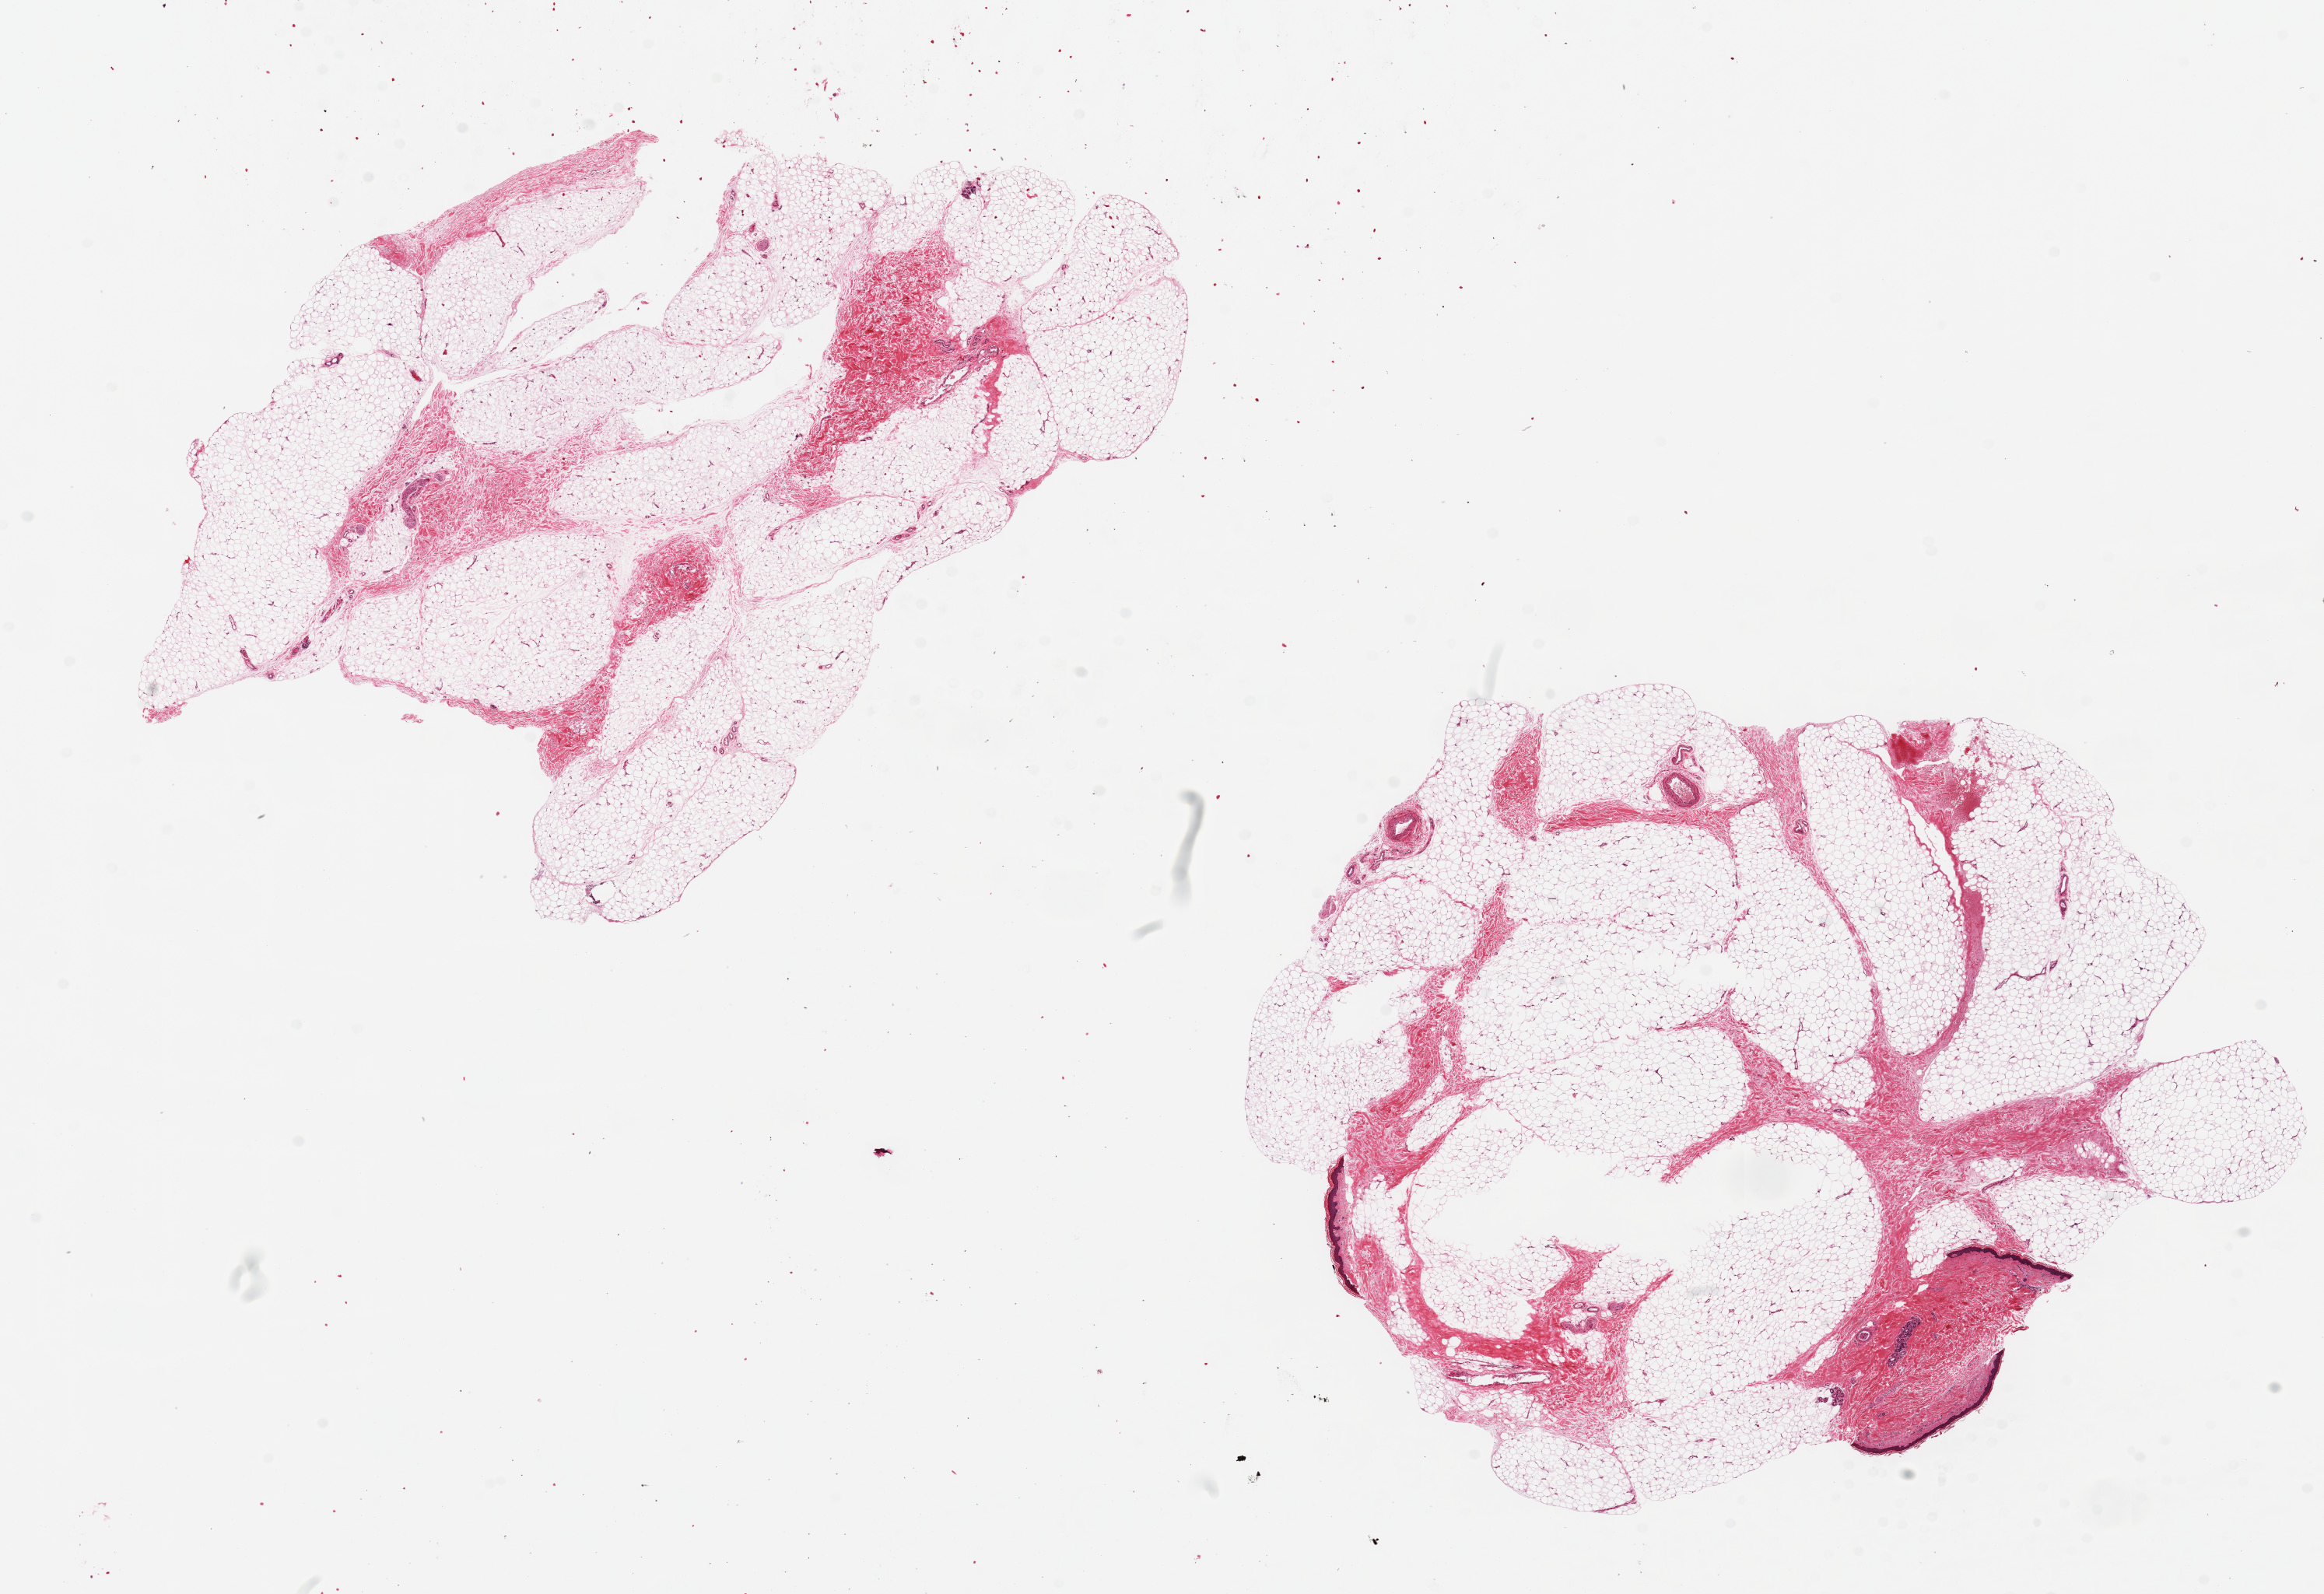
Haematoxylin and eosin whole-slide image — low-resolution overview of the scanned area, about 23.6 x 16.2 mm. PAXgene-fixed paraffin-embedded (PFPE) section. Sampled site (target tissue): adipose tissue. Donor tissue sample. Donor sex: male.
Review note (as recorded): 2 pieces ~9x7mm; Contaminant fragements of skin present.